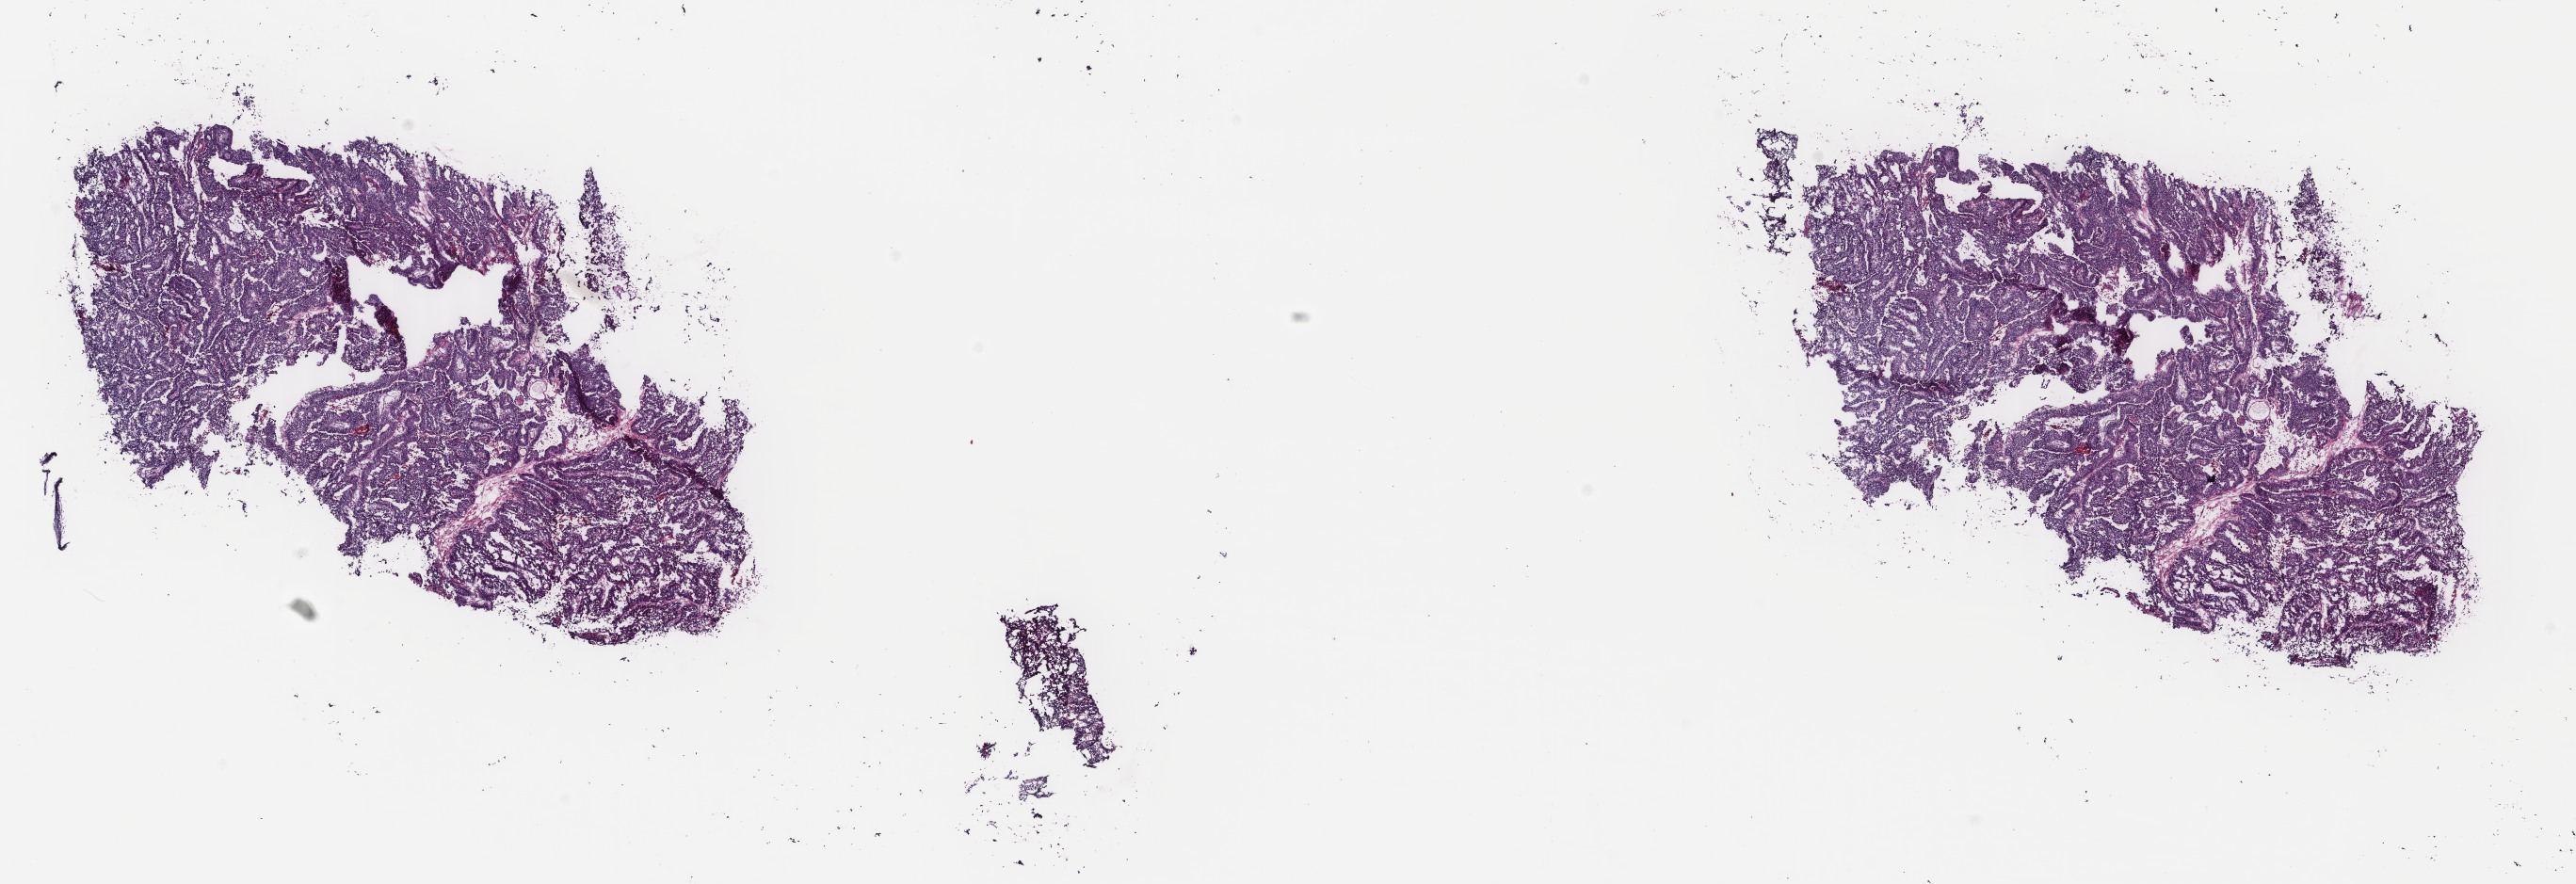
Whole-slide histology image, H&E-stained — whole scanned area (about 21.7 x 7.5 mm, slide scanned at 40x) shown as a low-resolution overview, frozen section, bladder, primary tumour sample. Female, age 52 years at initial diagnosis. Histologic grade: high grade. Pathologist review of this section (percent, as recorded): tumour cells 100%, tumour nuclei 90%, normal cells 0%, stromal cells 0%, necrosis 0%. Infiltration values recorded for this section: lymphocyte infiltration 0%, monocyte infiltration 0%, neutrophil infiltration 0%.
* diagnosis: Papillary adenocarcinoma, NOS (dome of bladder)
* lymph nodes positive (case pathology): 0 of 10 examined
* AJCC pathologic stage: III (6th edition)